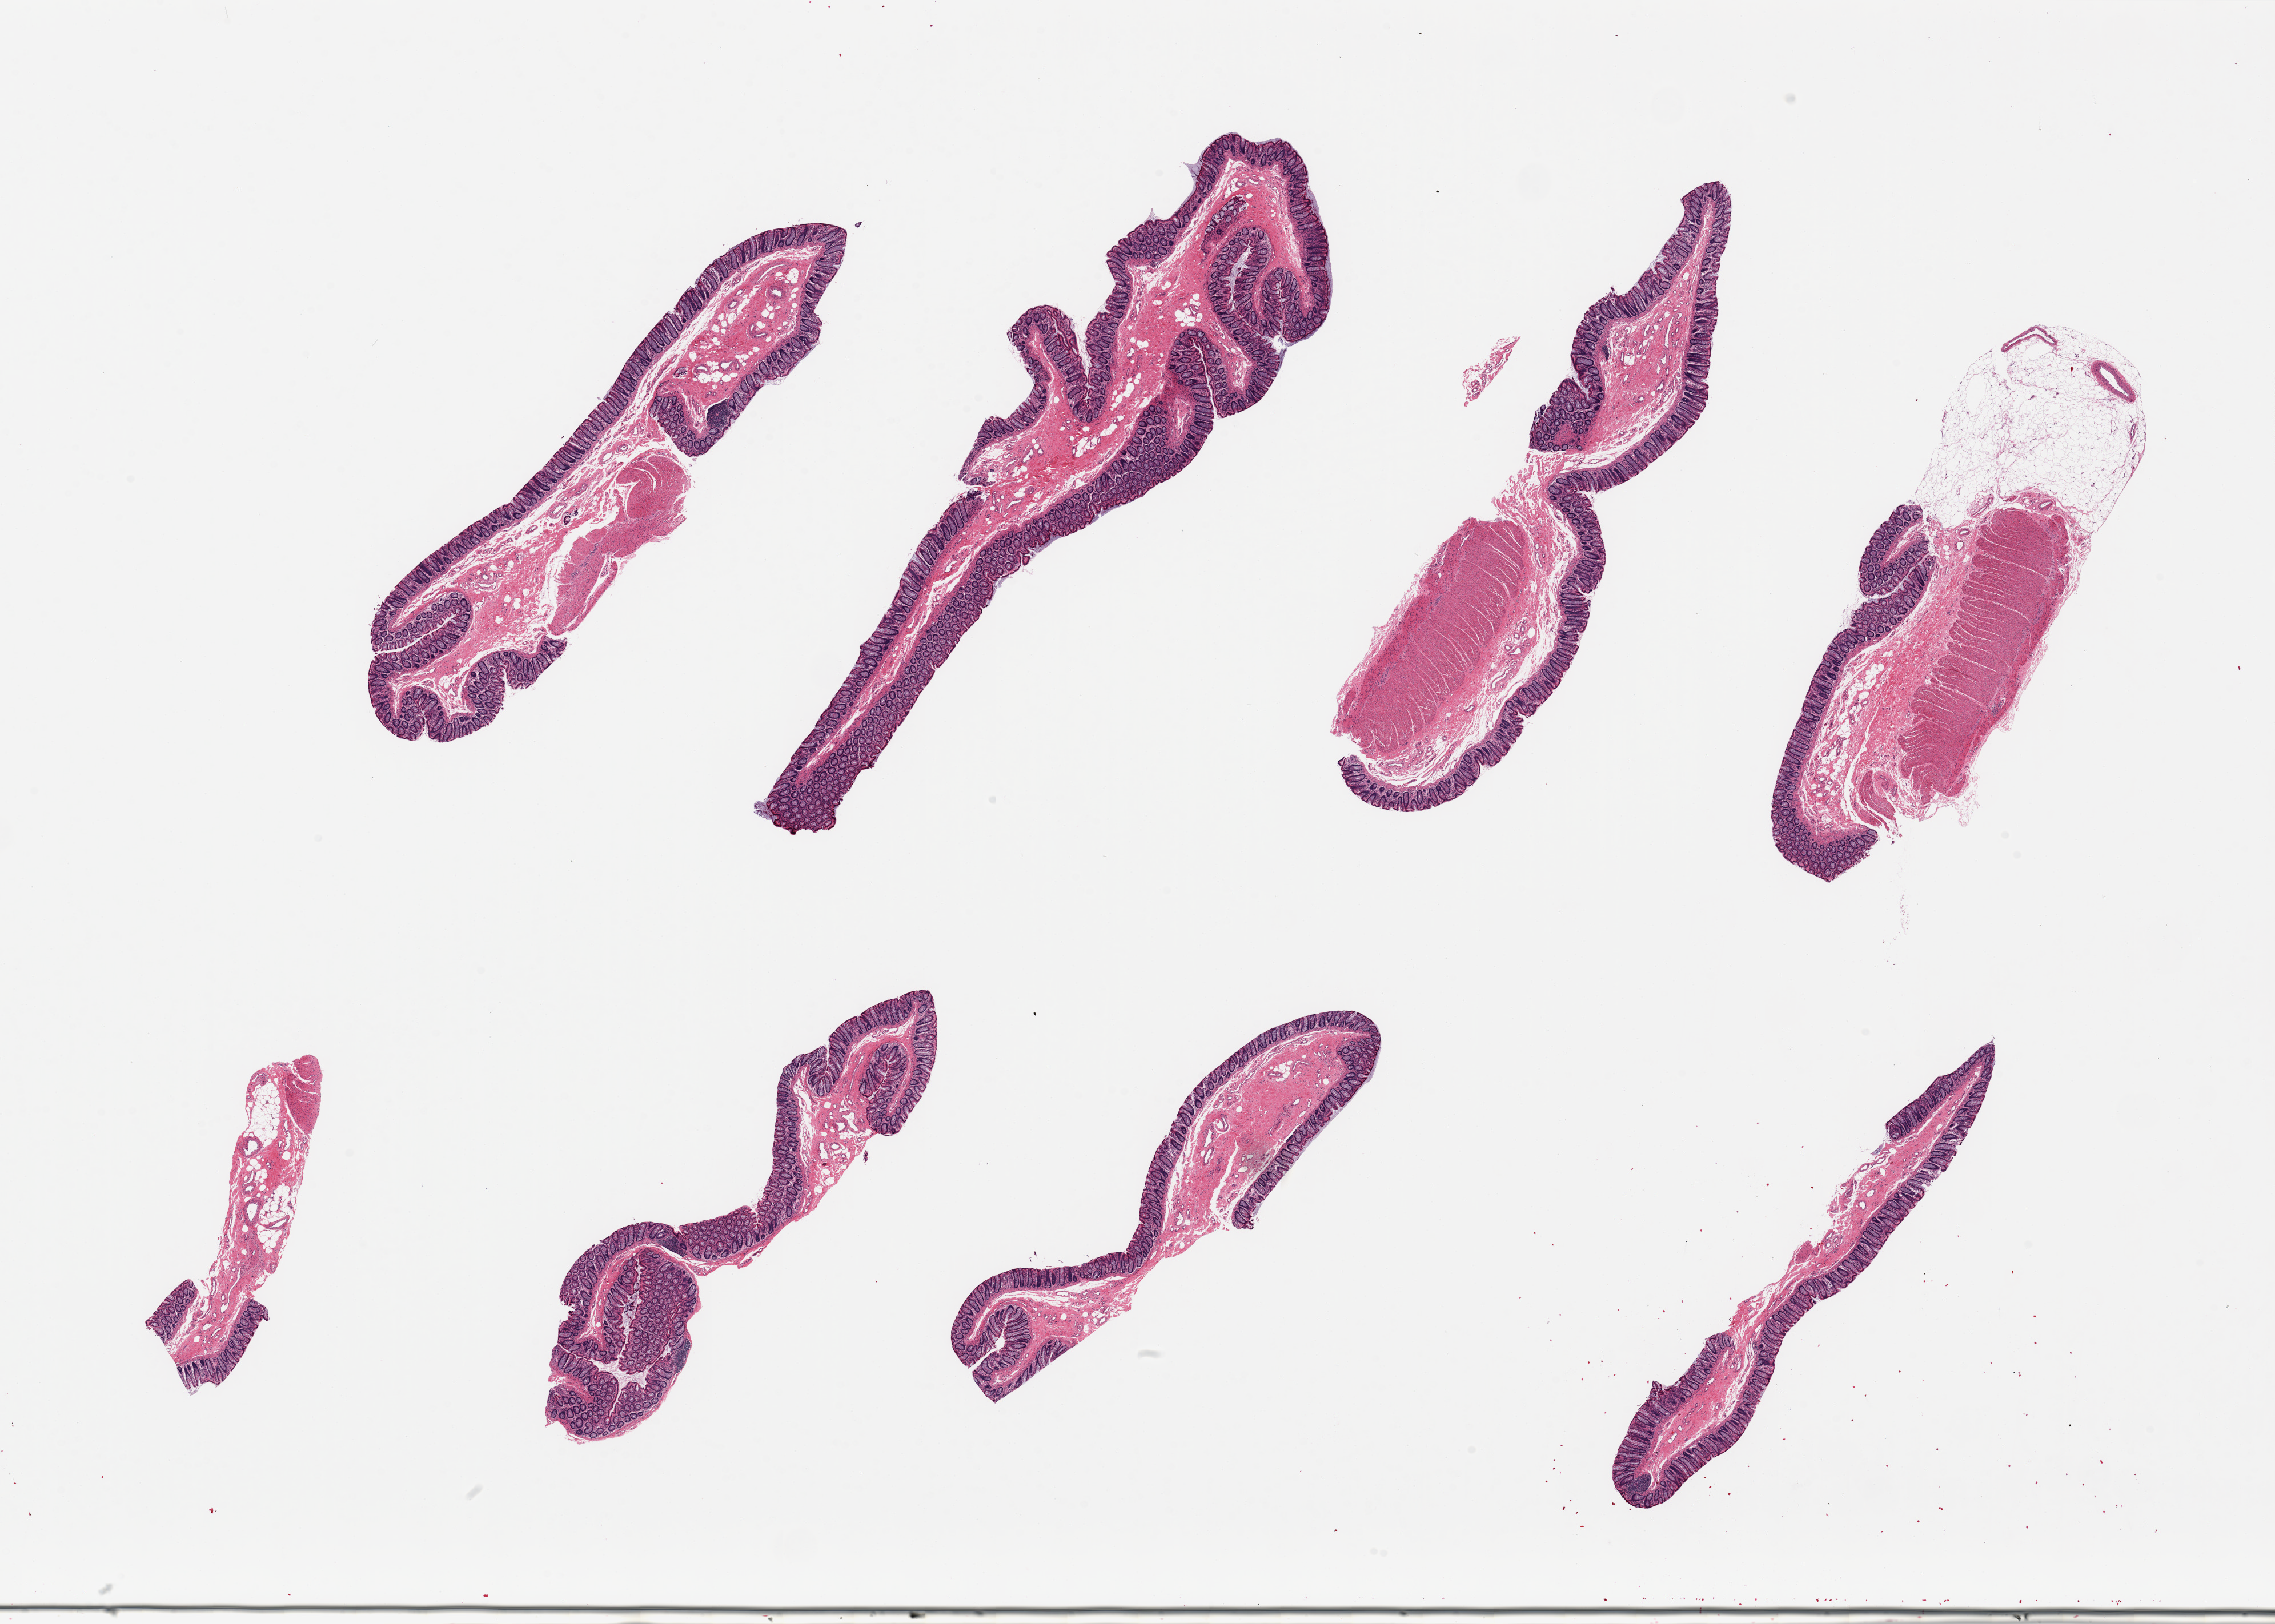
Digitized H&E-stained section — a low-resolution overview of the entire scanned area, about 31.5 x 22.5 mm (acquisition: 20x scan), PAXgene-fixed paraffin-embedded (PFPE) section, target tissue: transverse colon, donor tissue sample.
Reviewer comment on this tissue sample: 8 pieces ~10x2mm. Presumed transverse. Well-preserved mucosa is 10-20% thickness.